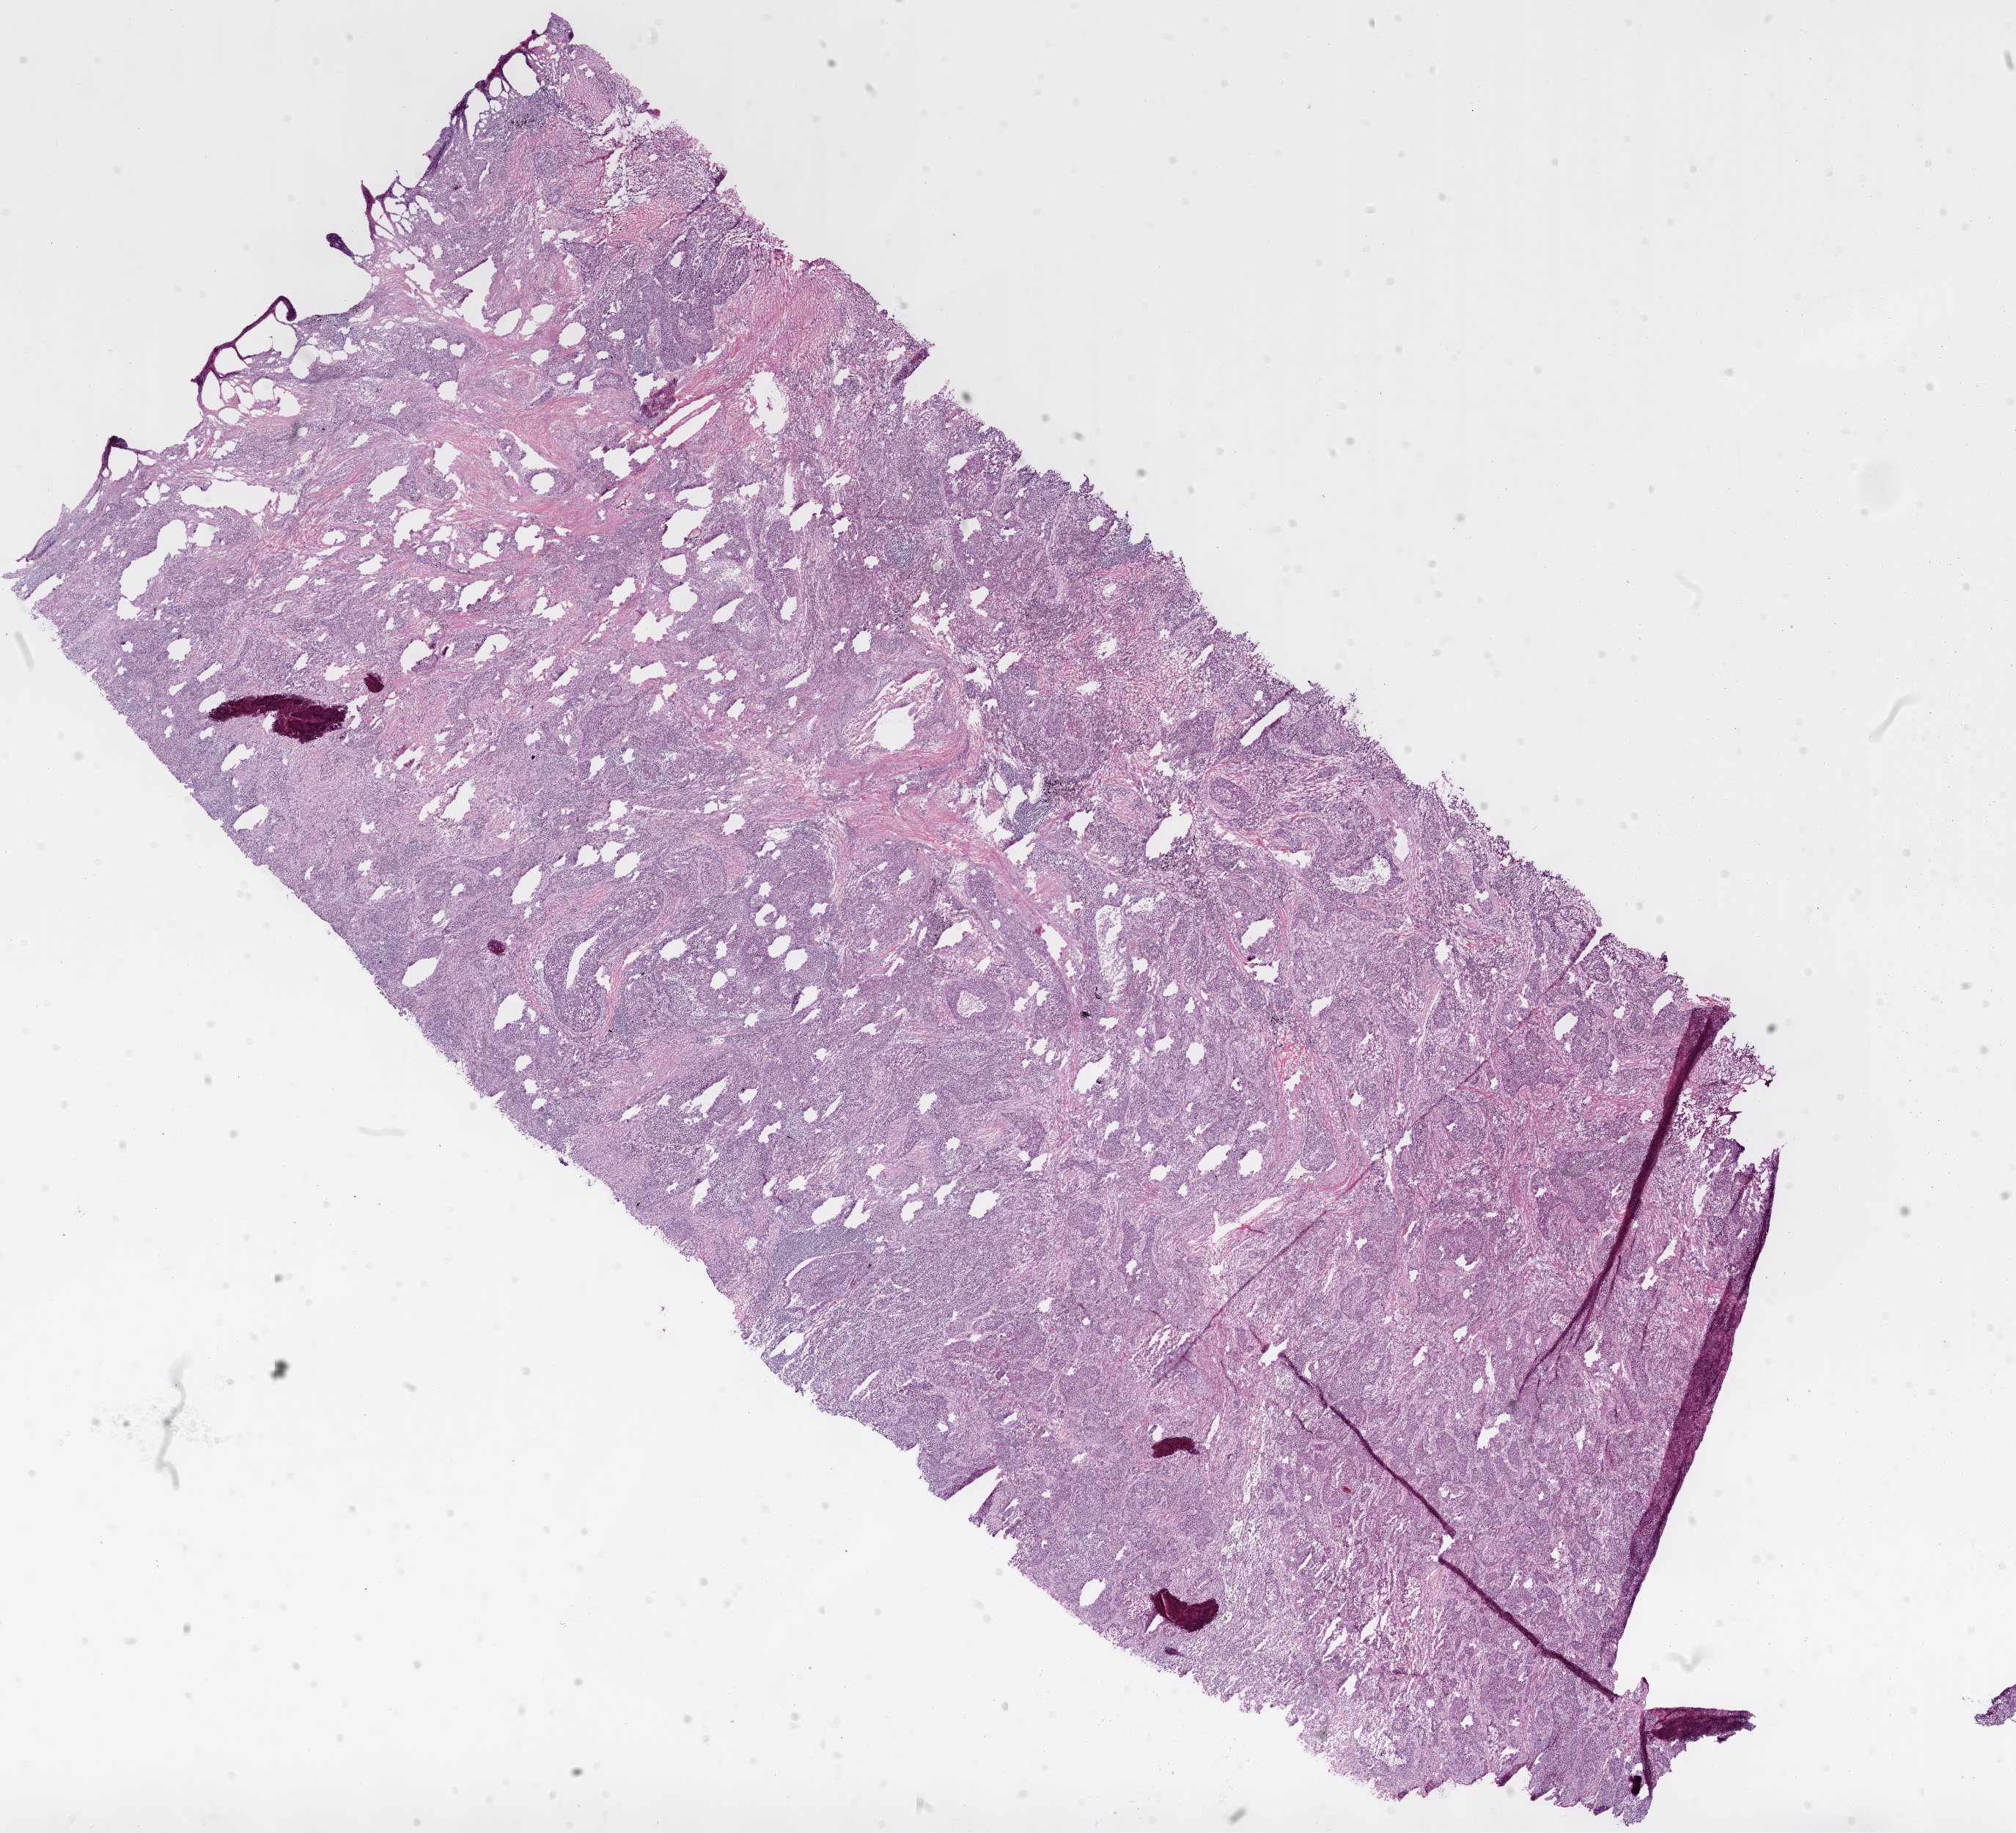
Digitized H&E tissue section (whole slide), a low-resolution overview of the entire scanned area, about 22.1 x 20.1 mm (slide scanned at 20x); frozen section from the bottom of the tissue portion; sample: primary tumour, lung. Patient: male, age at initial diagnosis 71 years. Composition of this section per pathologist review: tumour cells 74%, tumour nuclei 75%, normal cells 3%, stromal cells 15%, necrosis 8%.
AJCC pathologic stage: IIB (5th edition). TNM: T3 N0 M0. Laterality: right. Histologic diagnosis: Squamous cell carcinoma, NOS (upper lobe, lung).